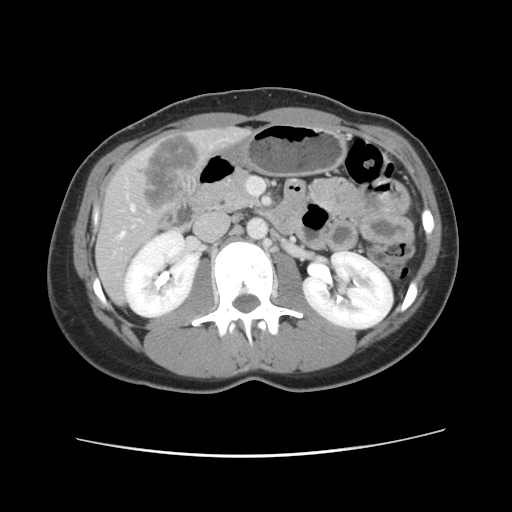
Contrast-enhanced abdominal CT, one axial slice; slice 40 of 134 in the series (ordered by position); 120 kVp; intravenous contrast given; soft-tissue window (W 400 / L 40 HU); 2.5 mm slice thickness; 512 × 512 image matrix, field of view 339 × 339 mm. Female patient, age 33 years. Case-level facts recorded for this patient, not image findings: diagnosis: colorectal cancer liver metastases, imaged before liver resection; multiple liver metastases: yes; largest metastasis: 4.5 cm; disease in both lobes: yes.
Annotated regions visible in this slice (outlined manually by an expert reader):
- hepatic veins: box from (x=119, y=206) to (x=135, y=239) px
- liver: (x=96, y=128)–(x=248, y=304)
- planned liver remnant (the part of the liver to remain after resection): (x=96, y=240)–(x=129, y=304)
- liver metastasis: (x=138, y=135)–(x=200, y=210)